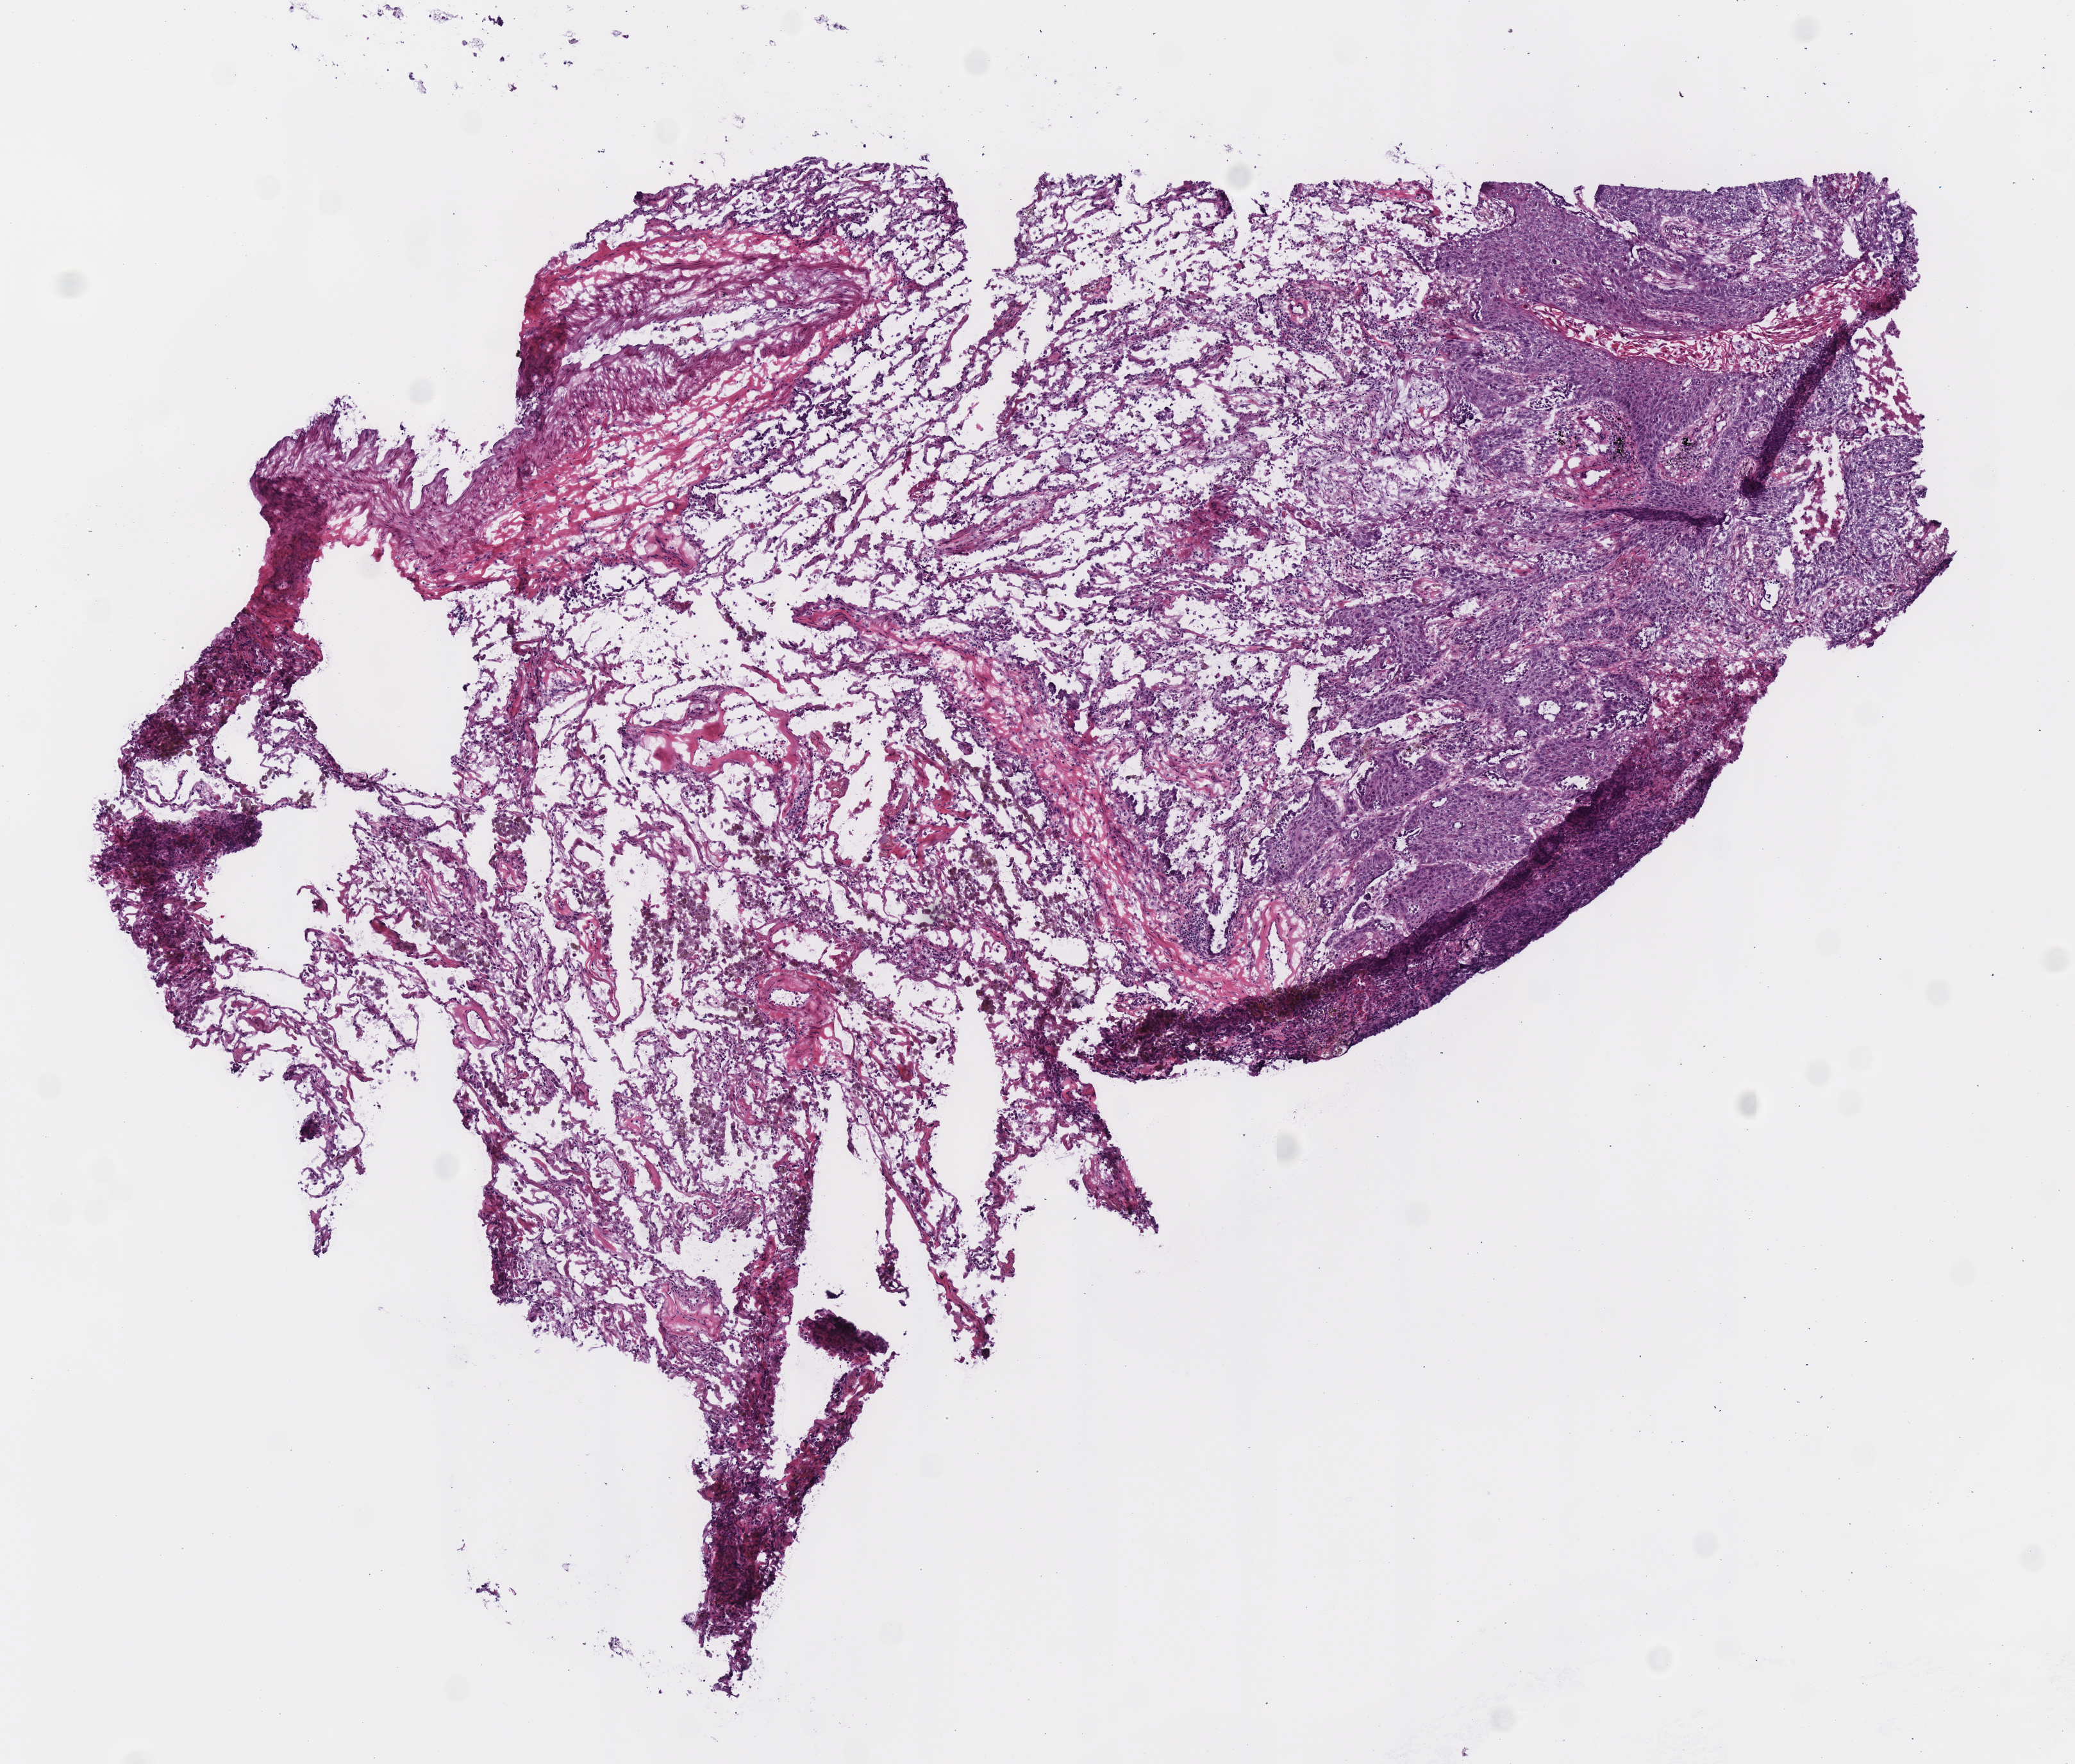
Digitized H&E-stained tissue section (whole slide), whole scanned area (about 6.4 x 5.4 mm) shown as a low-resolution overview. Frozen section from the bottom of the tissue portion. Primary tumour sample from the lung. Male, age 70 years at initial diagnosis. Slide review estimates, as recorded: tumour cells 30%, tumour nuclei 38%.
Diagnosis: Squamous cell carcinoma, NOS (upper lobe, lung).